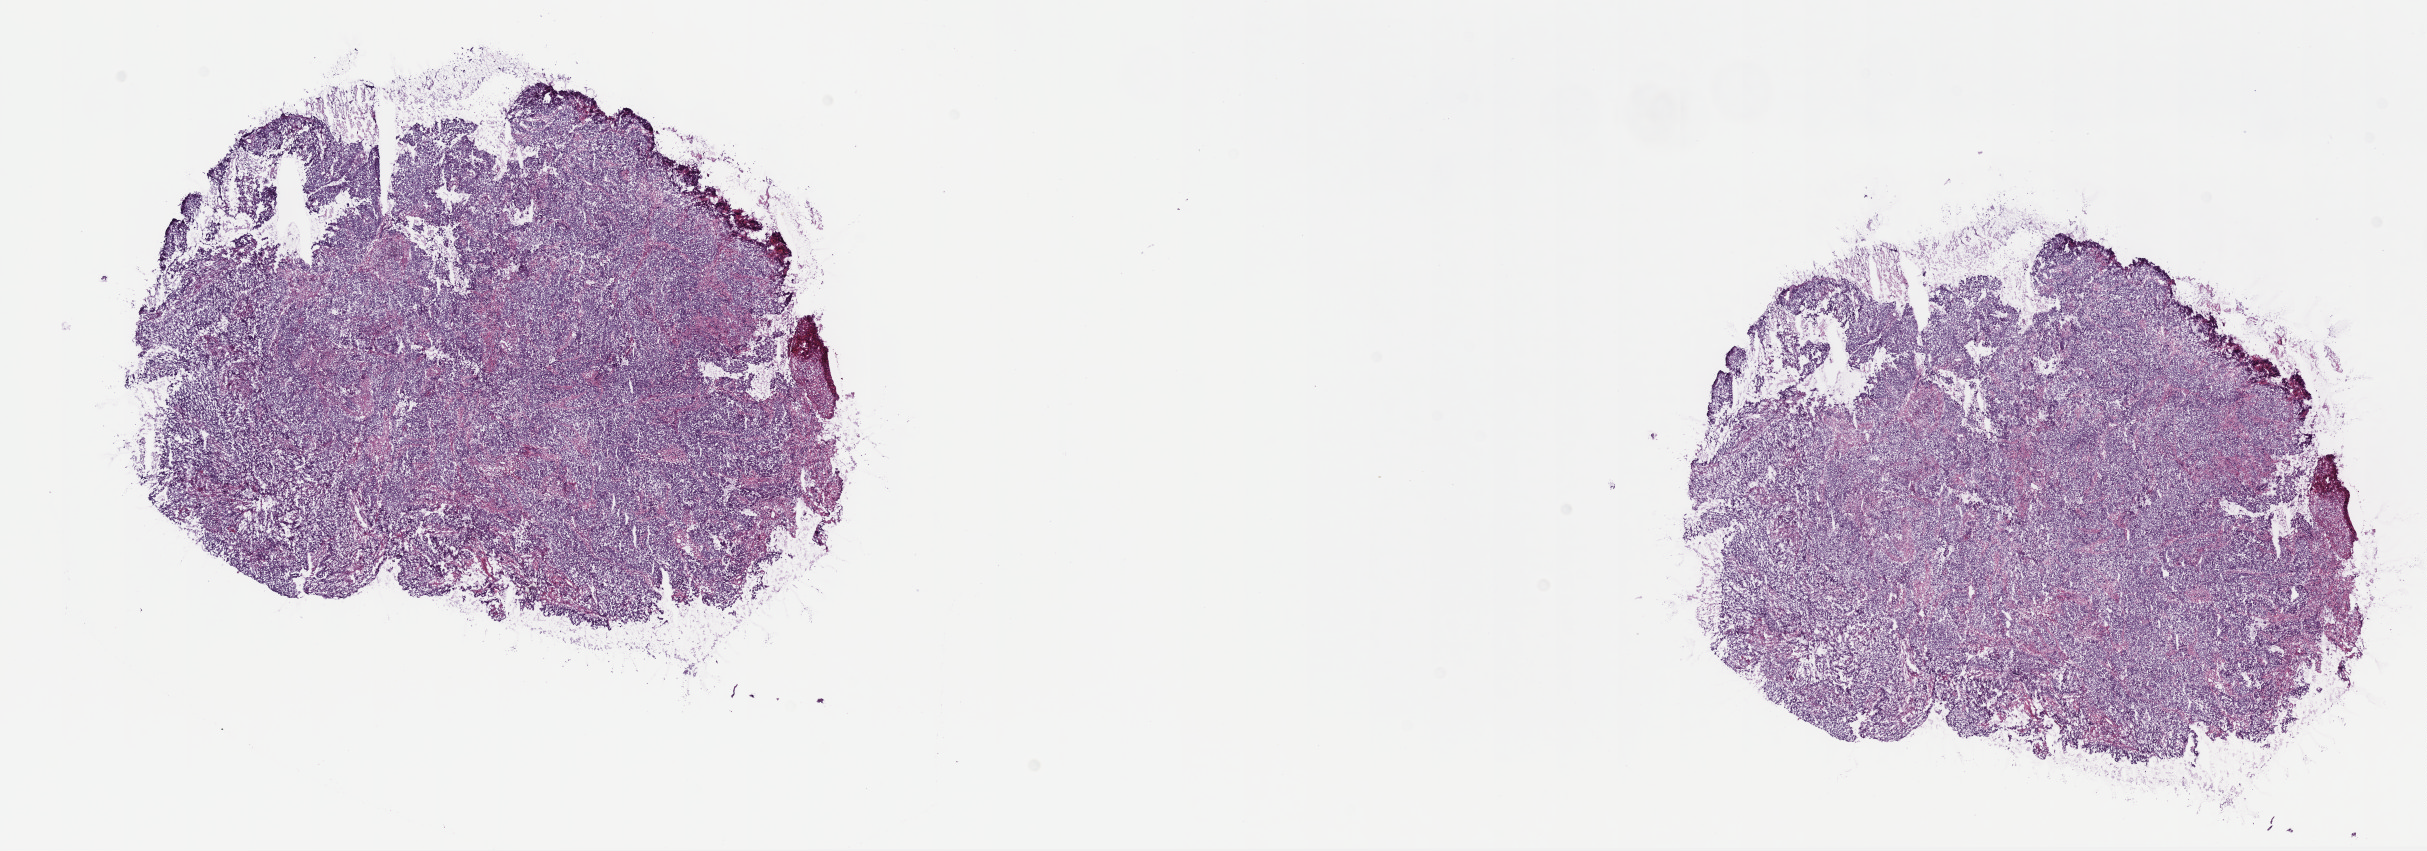
Digitized H&E-stained tissue section (whole slide) — shown as a low-resolution overview of the whole scanned area (about 19.6 x 6.9 mm, acquisition: 40x scan); frozen section from the top of the tissue portion; sample: primary tumour, cervix. Female, age 52 years at initial diagnosis. Histologic grade: GX (grade cannot be assessed). Composition of this section per pathologist review: tumour cells 80%, tumour nuclei 80%, normal cells 5%, stromal cells 15%, necrosis 0%. Infiltration values recorded for this section: lymphocyte infiltration 2%, monocyte infiltration 0%, neutrophil infiltration 0%.
Pathologic diagnosis: Squamous cell carcinoma, large cell, nonkeratinizing, NOS (cervix uteri). FIGO stage: IVB.